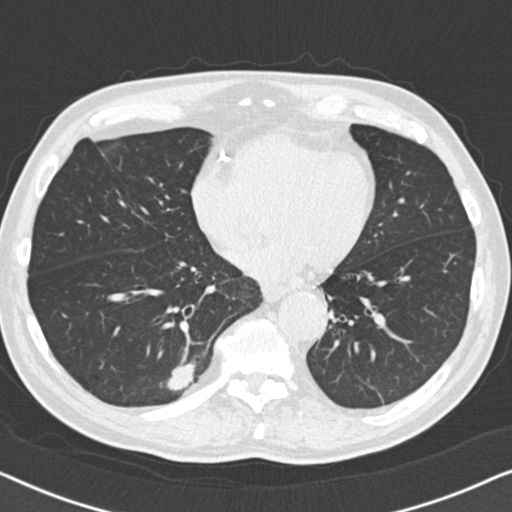
Chest CT (low-dose screening protocol), one axial image; second screening round (one year after baseline); lung window (W 1500 / L -600 HU); 2 mm slice thickness; standard (soft-tissue) reconstruction kernel (B30f); 120 kVp; 512 × 512 image matrix, field of view 330 × 330 mm. Male participant, aged 74 years at enrolment. Current smoker at enrolment.
Expert-annotated lung lesion, bounding box (x1, y1, x2, y2) in pixels: (149, 345, 218, 407). The screening reader recorded 5 non-calcified nodules or masses ≥4 mm on this exam; which of them this box marks is not recorded. Official screen result: positive, other. Lung cancer was diagnosed 55 days after this screen: bronchiolo-alveolar adenocarcinoma, NOS, right lower lobe, moderately differentiated (G2), stage IA (AJCC 6th edition), 16 mm at pathology.